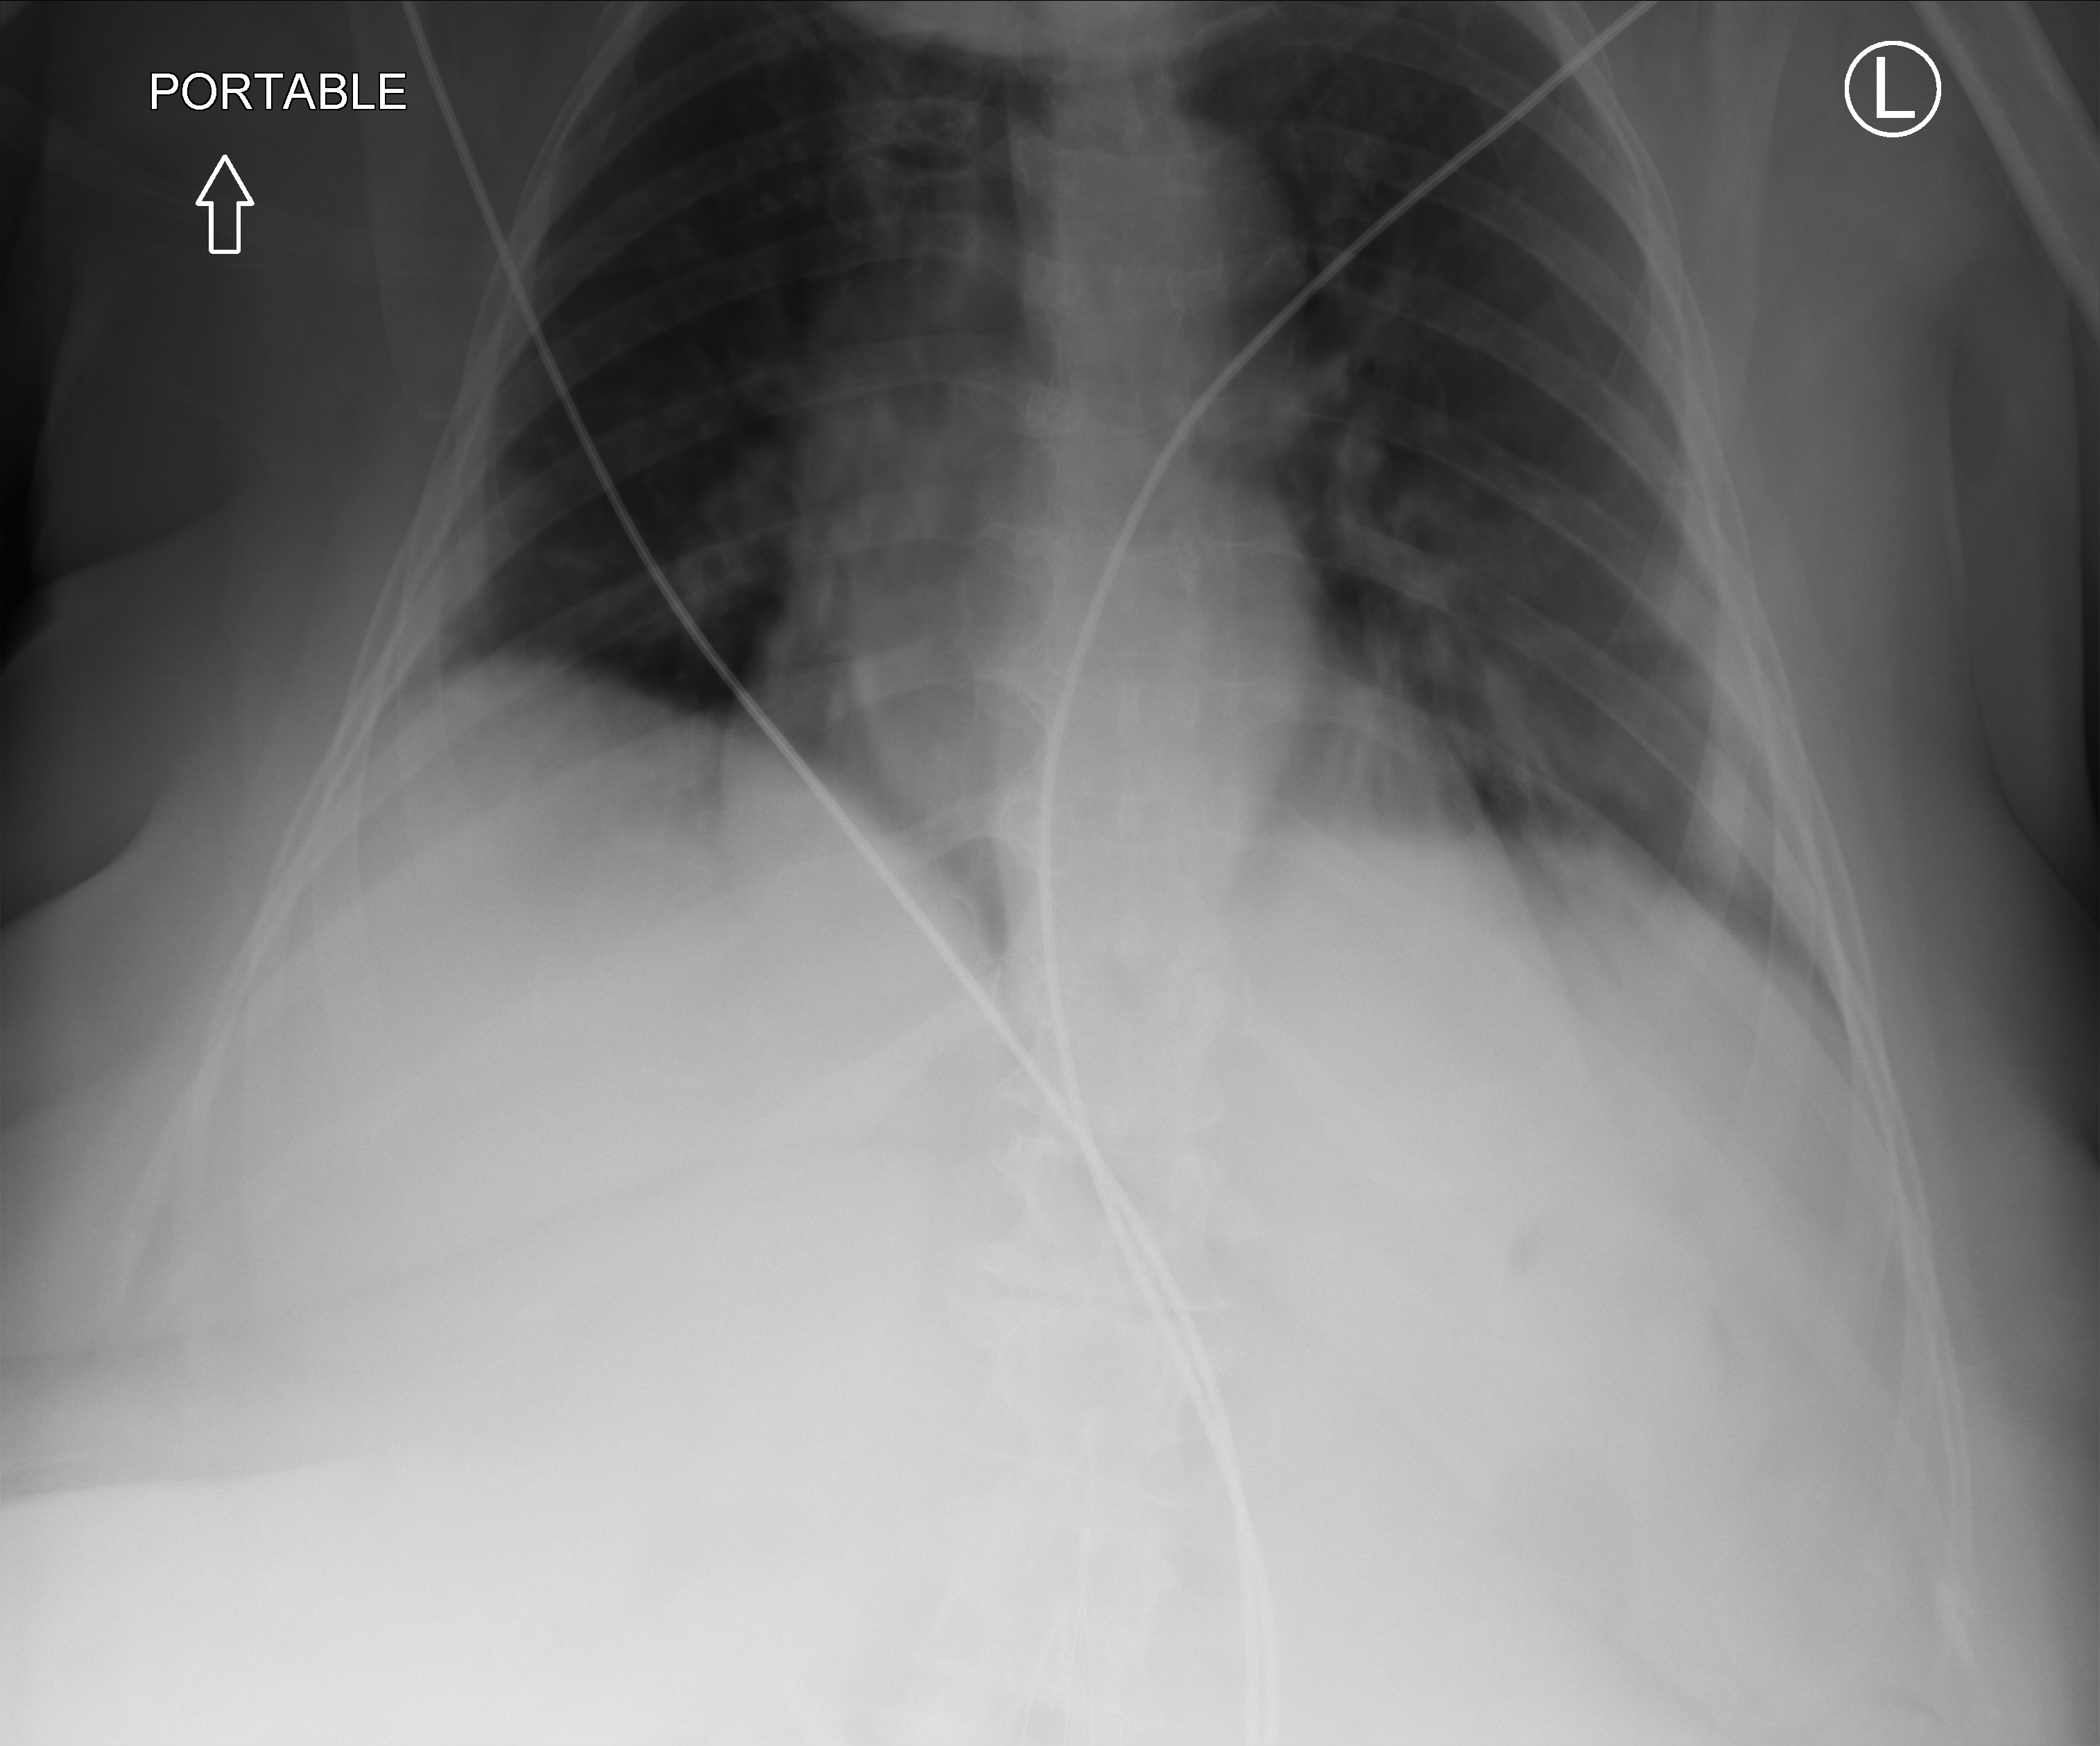
Bedside abdomen radiograph (computed radiography); anteroposterior (AP) projection. Female patient hospitalised with COVID-19, age 60–74 years.
Hospital-stay facts (about this admission, not read from this image; timing relative to this image not recorded): mechanically ventilated during this hospital stay: no.